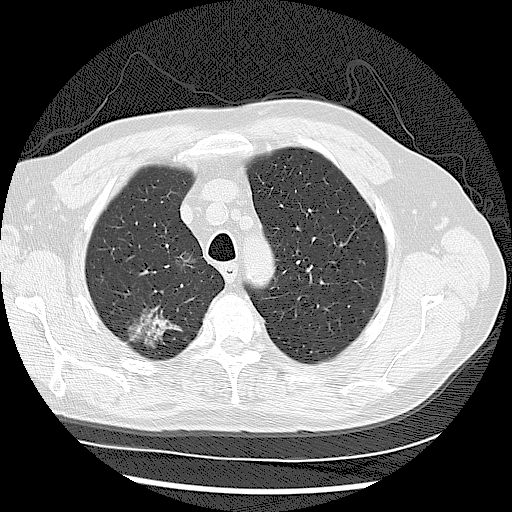
Low-dose screening chest CT, one axial slice; position 93 of 122 along the scan axis; reconstruction kernel LUNG; 120 kVp; lung window (W 1500 / L -600 HU); 2.5 mm slice thickness; 512 × 512 image matrix.
Annotated regions visible in this slice (manually delineated by an expert):
- lesion 1 (tumor, upper lobe of right lung): bounding box [x1, y1, x2, y2] px = [130, 309, 181, 346]